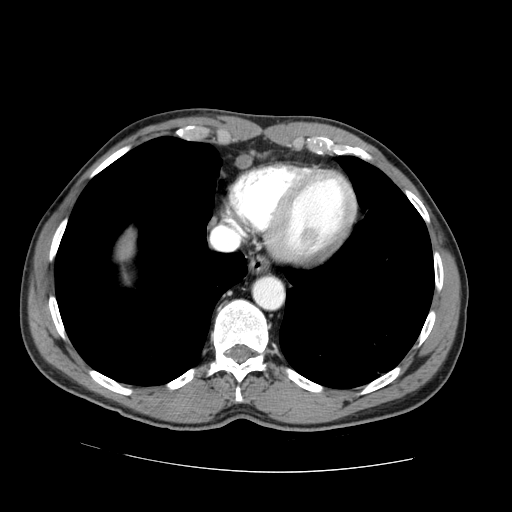
Contrast-enhanced abdominal CT (liver protocol), one axial slice; position 67 of 73 along the scan axis; 100 kVp; one of 2 acquisitions stored at this slice position; soft-tissue window (W 400 / L 40 HU); 2.5 mm slice thickness; 512 × 512 image matrix, field of view 380 × 380 mm. Case-level facts recorded for this patient, not image findings: diagnosis: hepatocellular carcinoma (patient treated with transarterial chemoembolisation; whether this scan precedes or follows treatment is not stated here); TNM stage (as recorded): Stage-IVA; Child-Pugh class: A; tumour differentiation: no biopsy; tumour nodularity: uninodular.
Outlined on this slice (semi-automatic segmentation, software-assisted and operator-edited):
- abdominal aorta: bounding box <254,277,283,309> (left, top, right, bottom; pixels)
- liver parenchyma outside the tumour (the mass and vessels are separate outlines, so this box may not span the whole liver): <118,234,134,260>